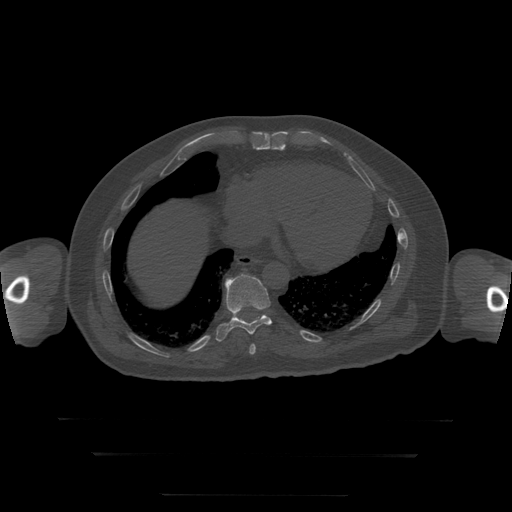
CT including the spine, one axial slice. Slice 123 of 397 in the series (ordered by position). Reconstruction kernel STANDARD. Bone window (W 1800 / L 400 HU). 1.25 mm slice thickness. 512 × 512 image matrix. Patient age 73 years. From the clinical record (not read from this slice): primary cancer: prostate.
Outlined on this slice (semi-automatic segmentation, software-assisted and operator-edited):
- T10 vertebra: bounding box [x1, y1, x2, y2] px = [216, 274, 272, 342]
- T9 vertebra: [249, 345, 256, 355]